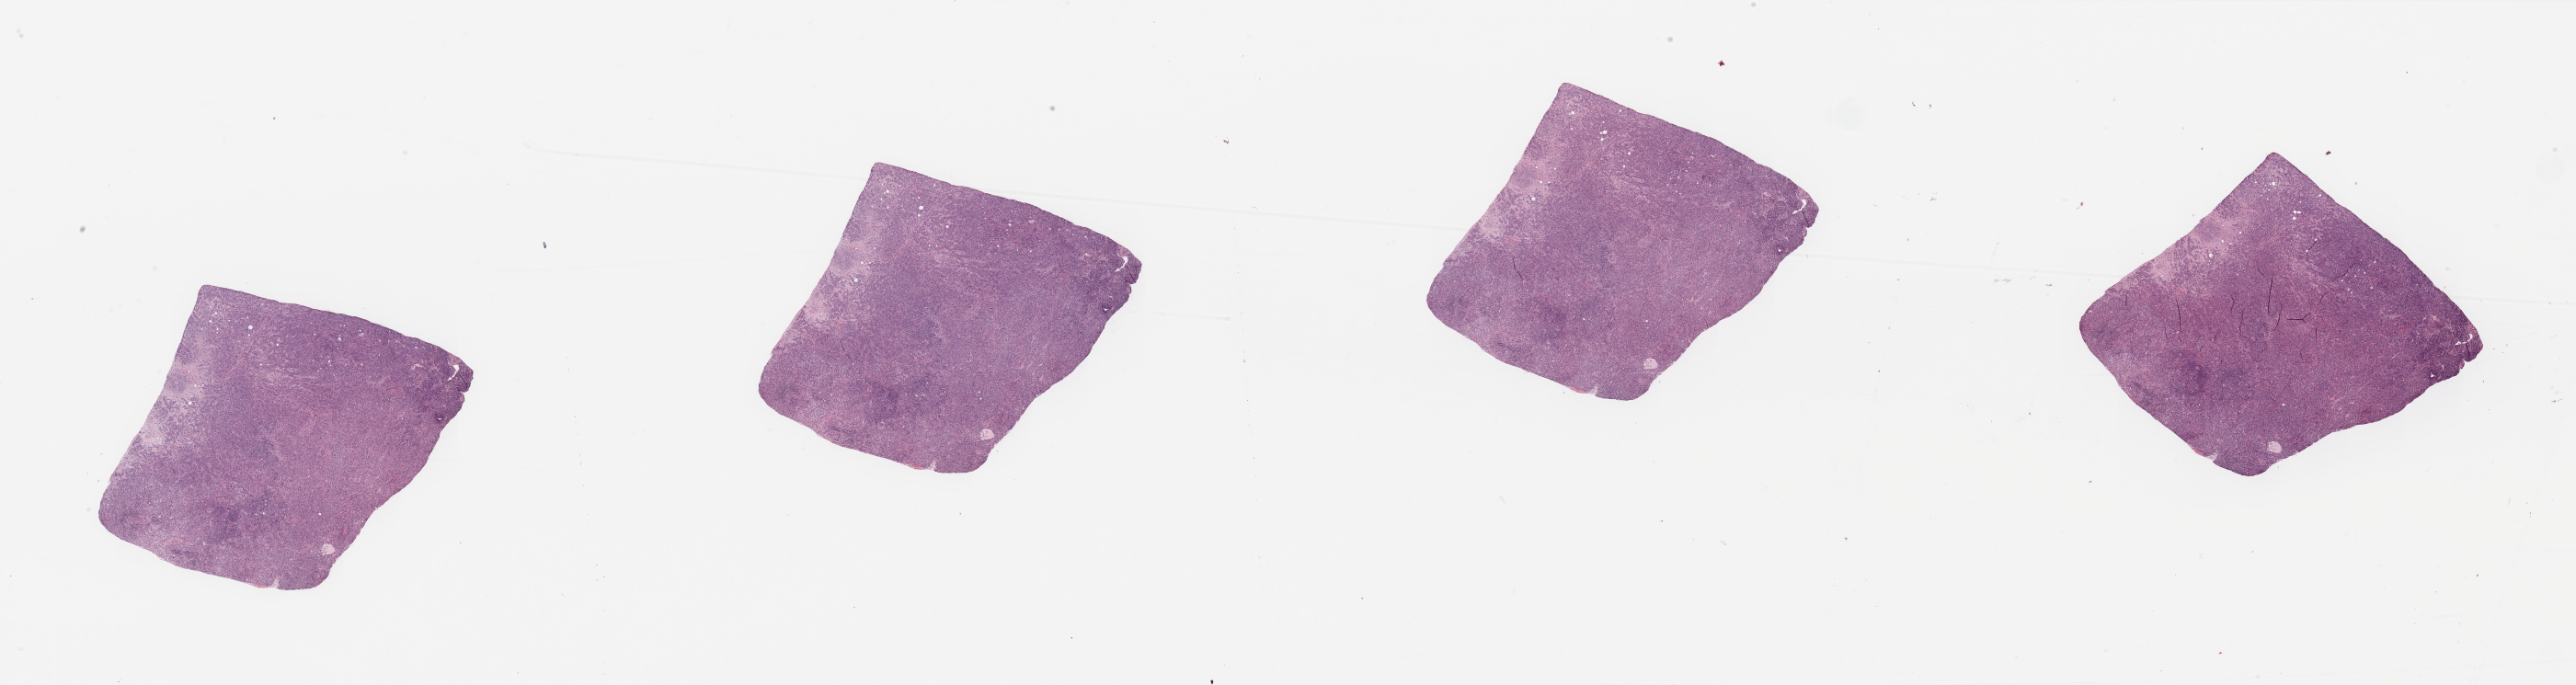
Digitized Hematoxylin and eosin (H&E) stained tissue section (whole slide), low-resolution overview of the scanned area, about 44.3 x 11.8 mm, tumour tissue sample, sampled site: pancreas. 76-year-old male patient. Histologic grade: G3 (poorly differentiated). Composition of this section per pathologist review: tumour nuclei 50%, necrosis 10%.
Primary tumour site (as recorded): head. AJCC pathologic stage: IB. Histologic diagnosis: Infiltrating duct carcinoma, NOS.